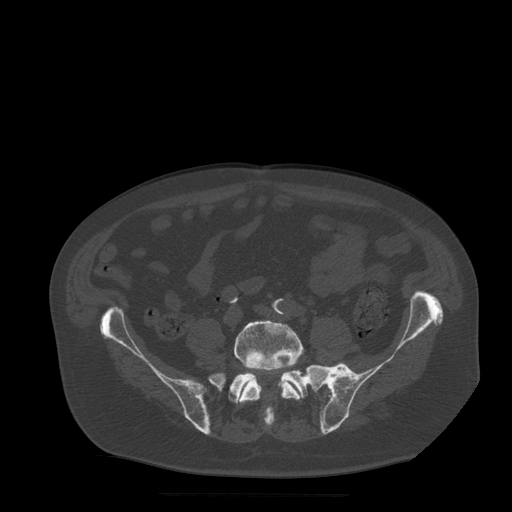
CT including the spine, one axial slice; slice 81 of 522 in the series (ordered by position); bone window (W 1800 / L 400 HU); 1.25 mm slice thickness; 512 × 512 image matrix, field of view 420 × 420 mm. Patient age 72 years. From the clinical record (not read from this slice): primary cancer: prostate.
Structures marked on this image (semi-automatic segmentation, software-assisted and operator-edited):
- L5 vertebra: bounding box (x1, y1, x2, y2) in pixels: (234, 320, 303, 421)